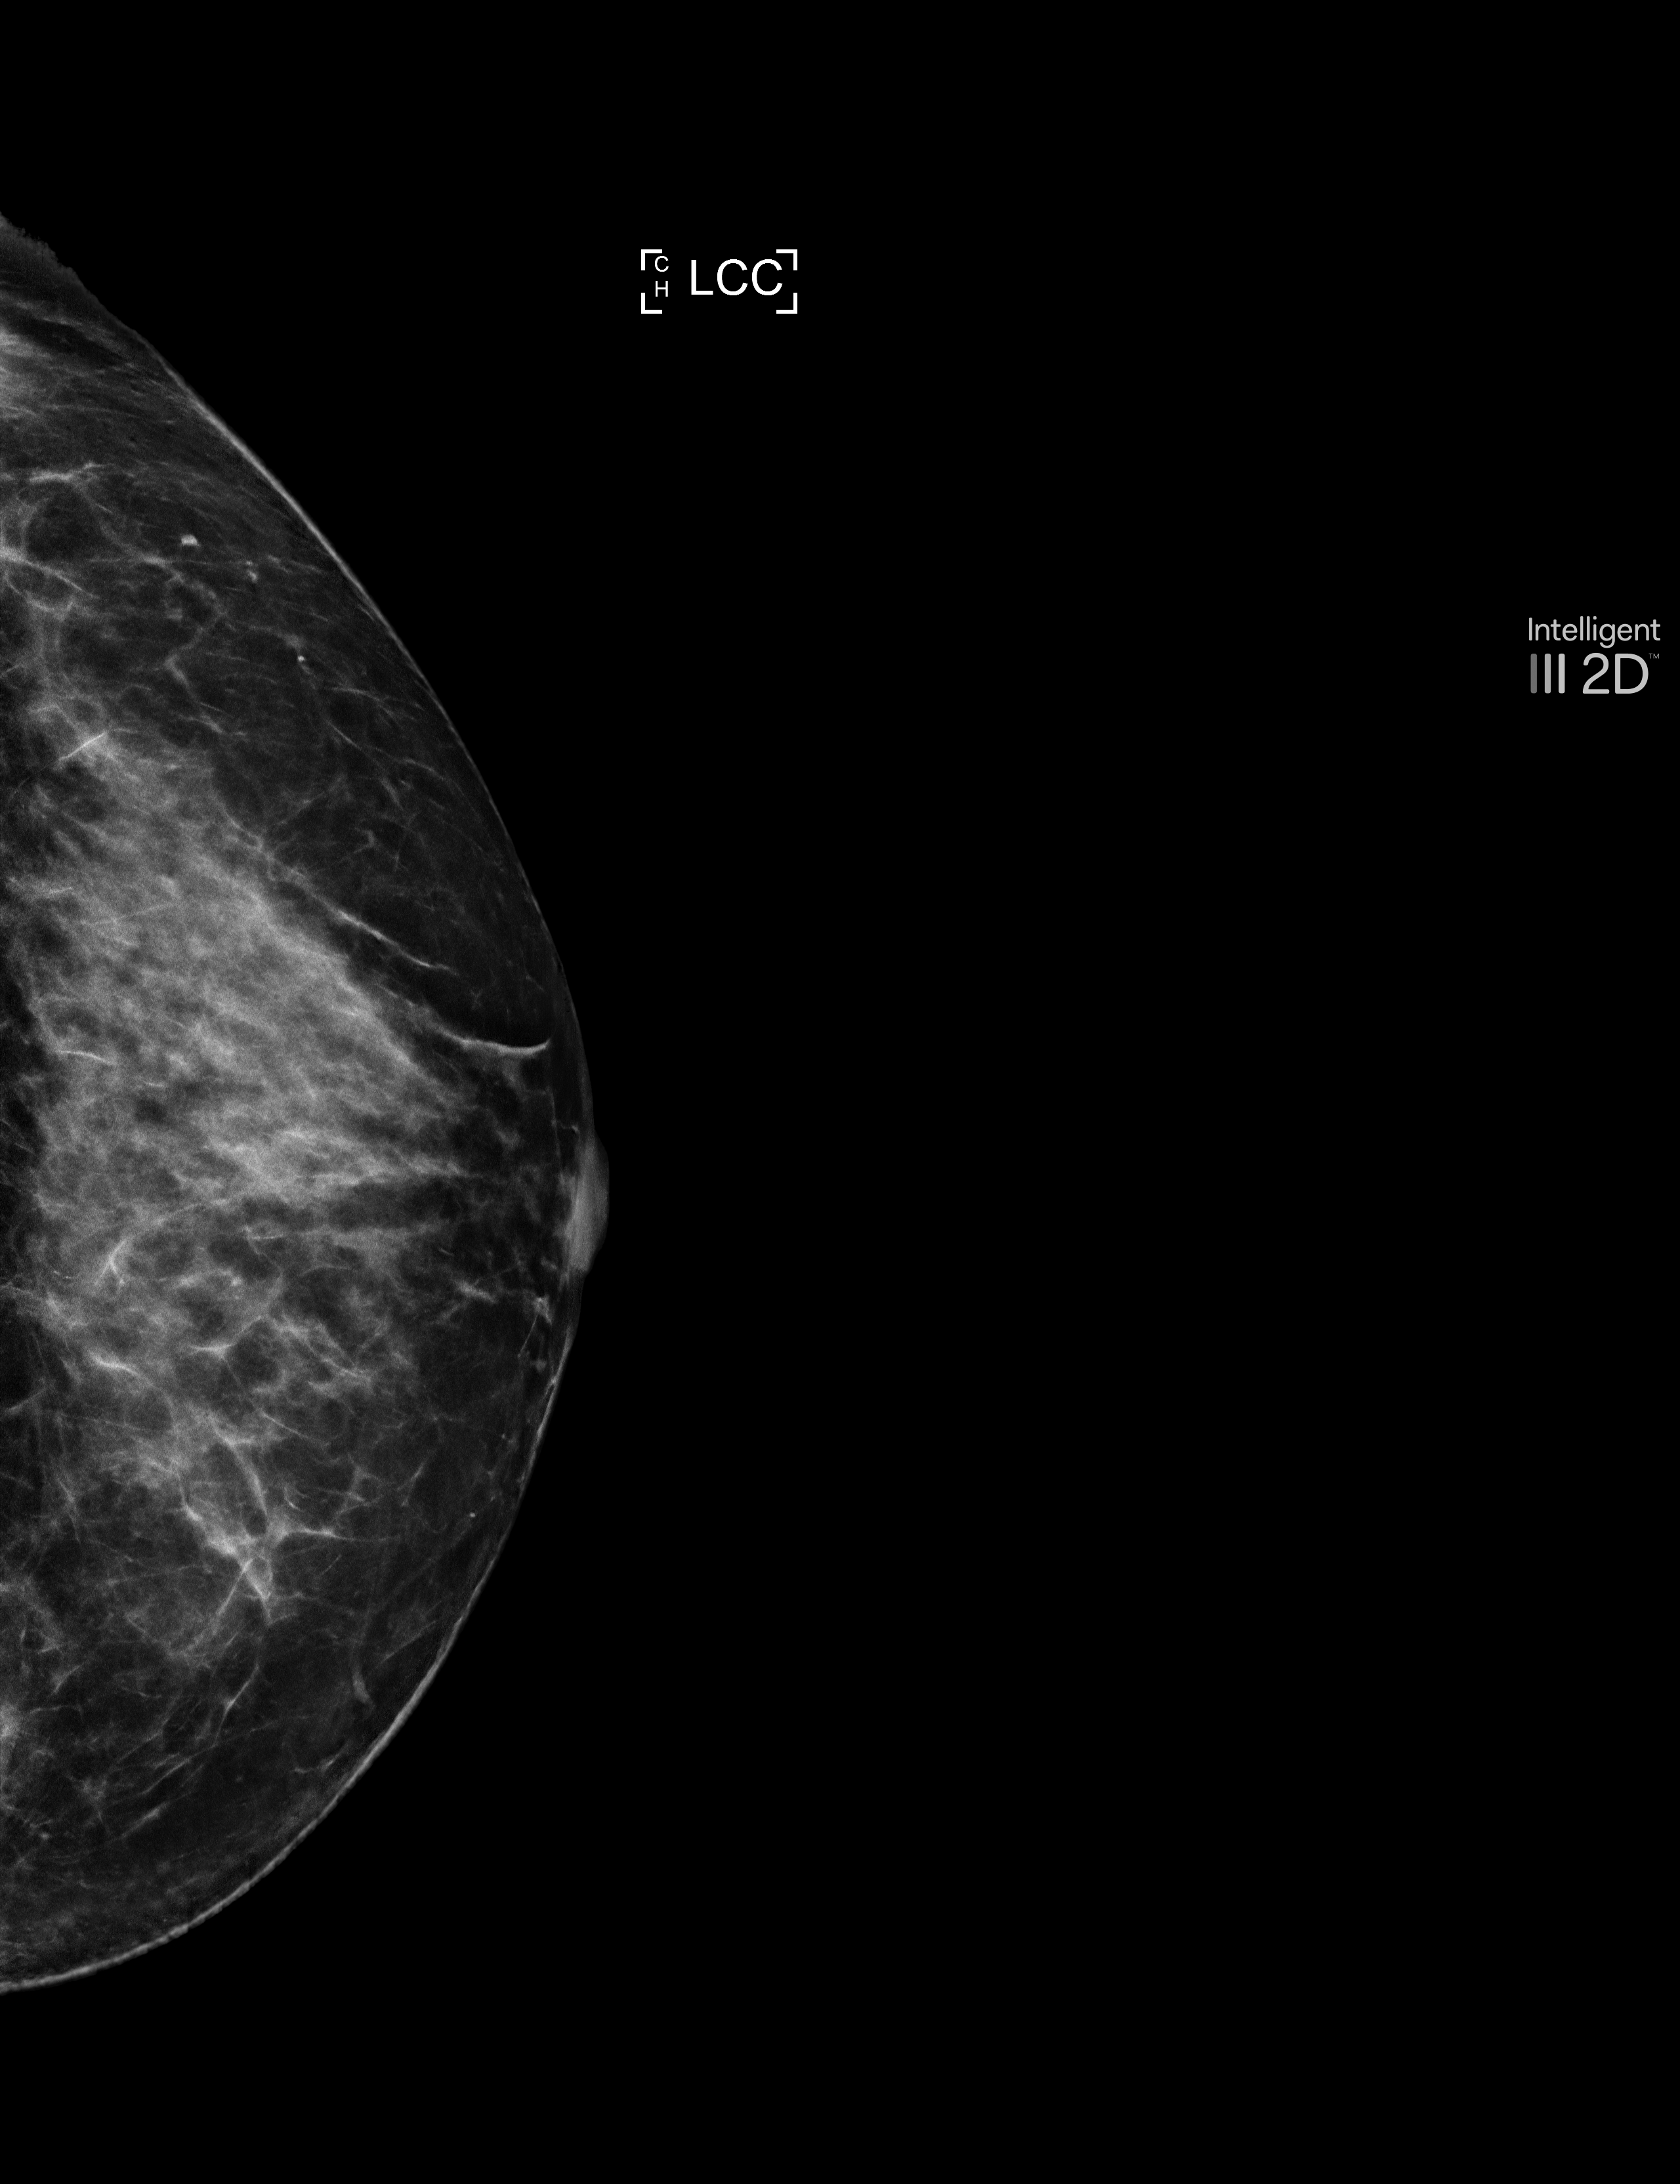
Annual screening mammography examination. Female patient, age 60 years.
Image type: synthesized 2-D view from tomosynthesis. Breast: left. Projection: craniocaudal (CC) view.